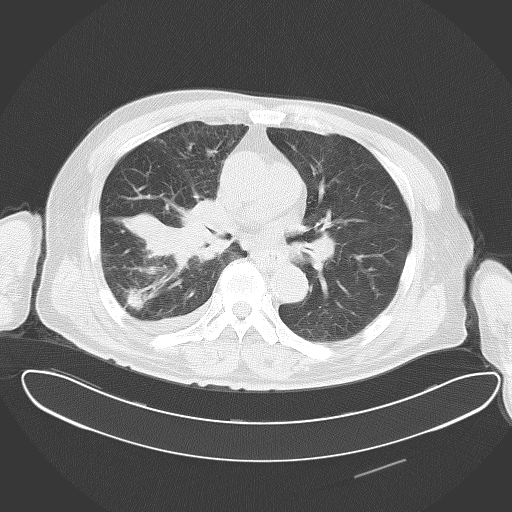
Chest CT, one axial slice. Position 31 of 62 along the scan axis. Reconstruction kernel B70f. 120 kVp. Lung window (W 1500 / L -600 HU). 5 mm slice thickness. 512 × 512 image matrix, field of view 427 × 427 mm. Patient: male, 78 years. Case-level facts recorded for this patient, not image findings: clinical TNM (as recorded): T2 N1 M1.
Structures marked on this image (rectangle marked by the reading radiologist):
- lung tumour (recorded histology: adenocarcinoma): bounding box <112,186,246,281> (left, top, right, bottom; pixels)